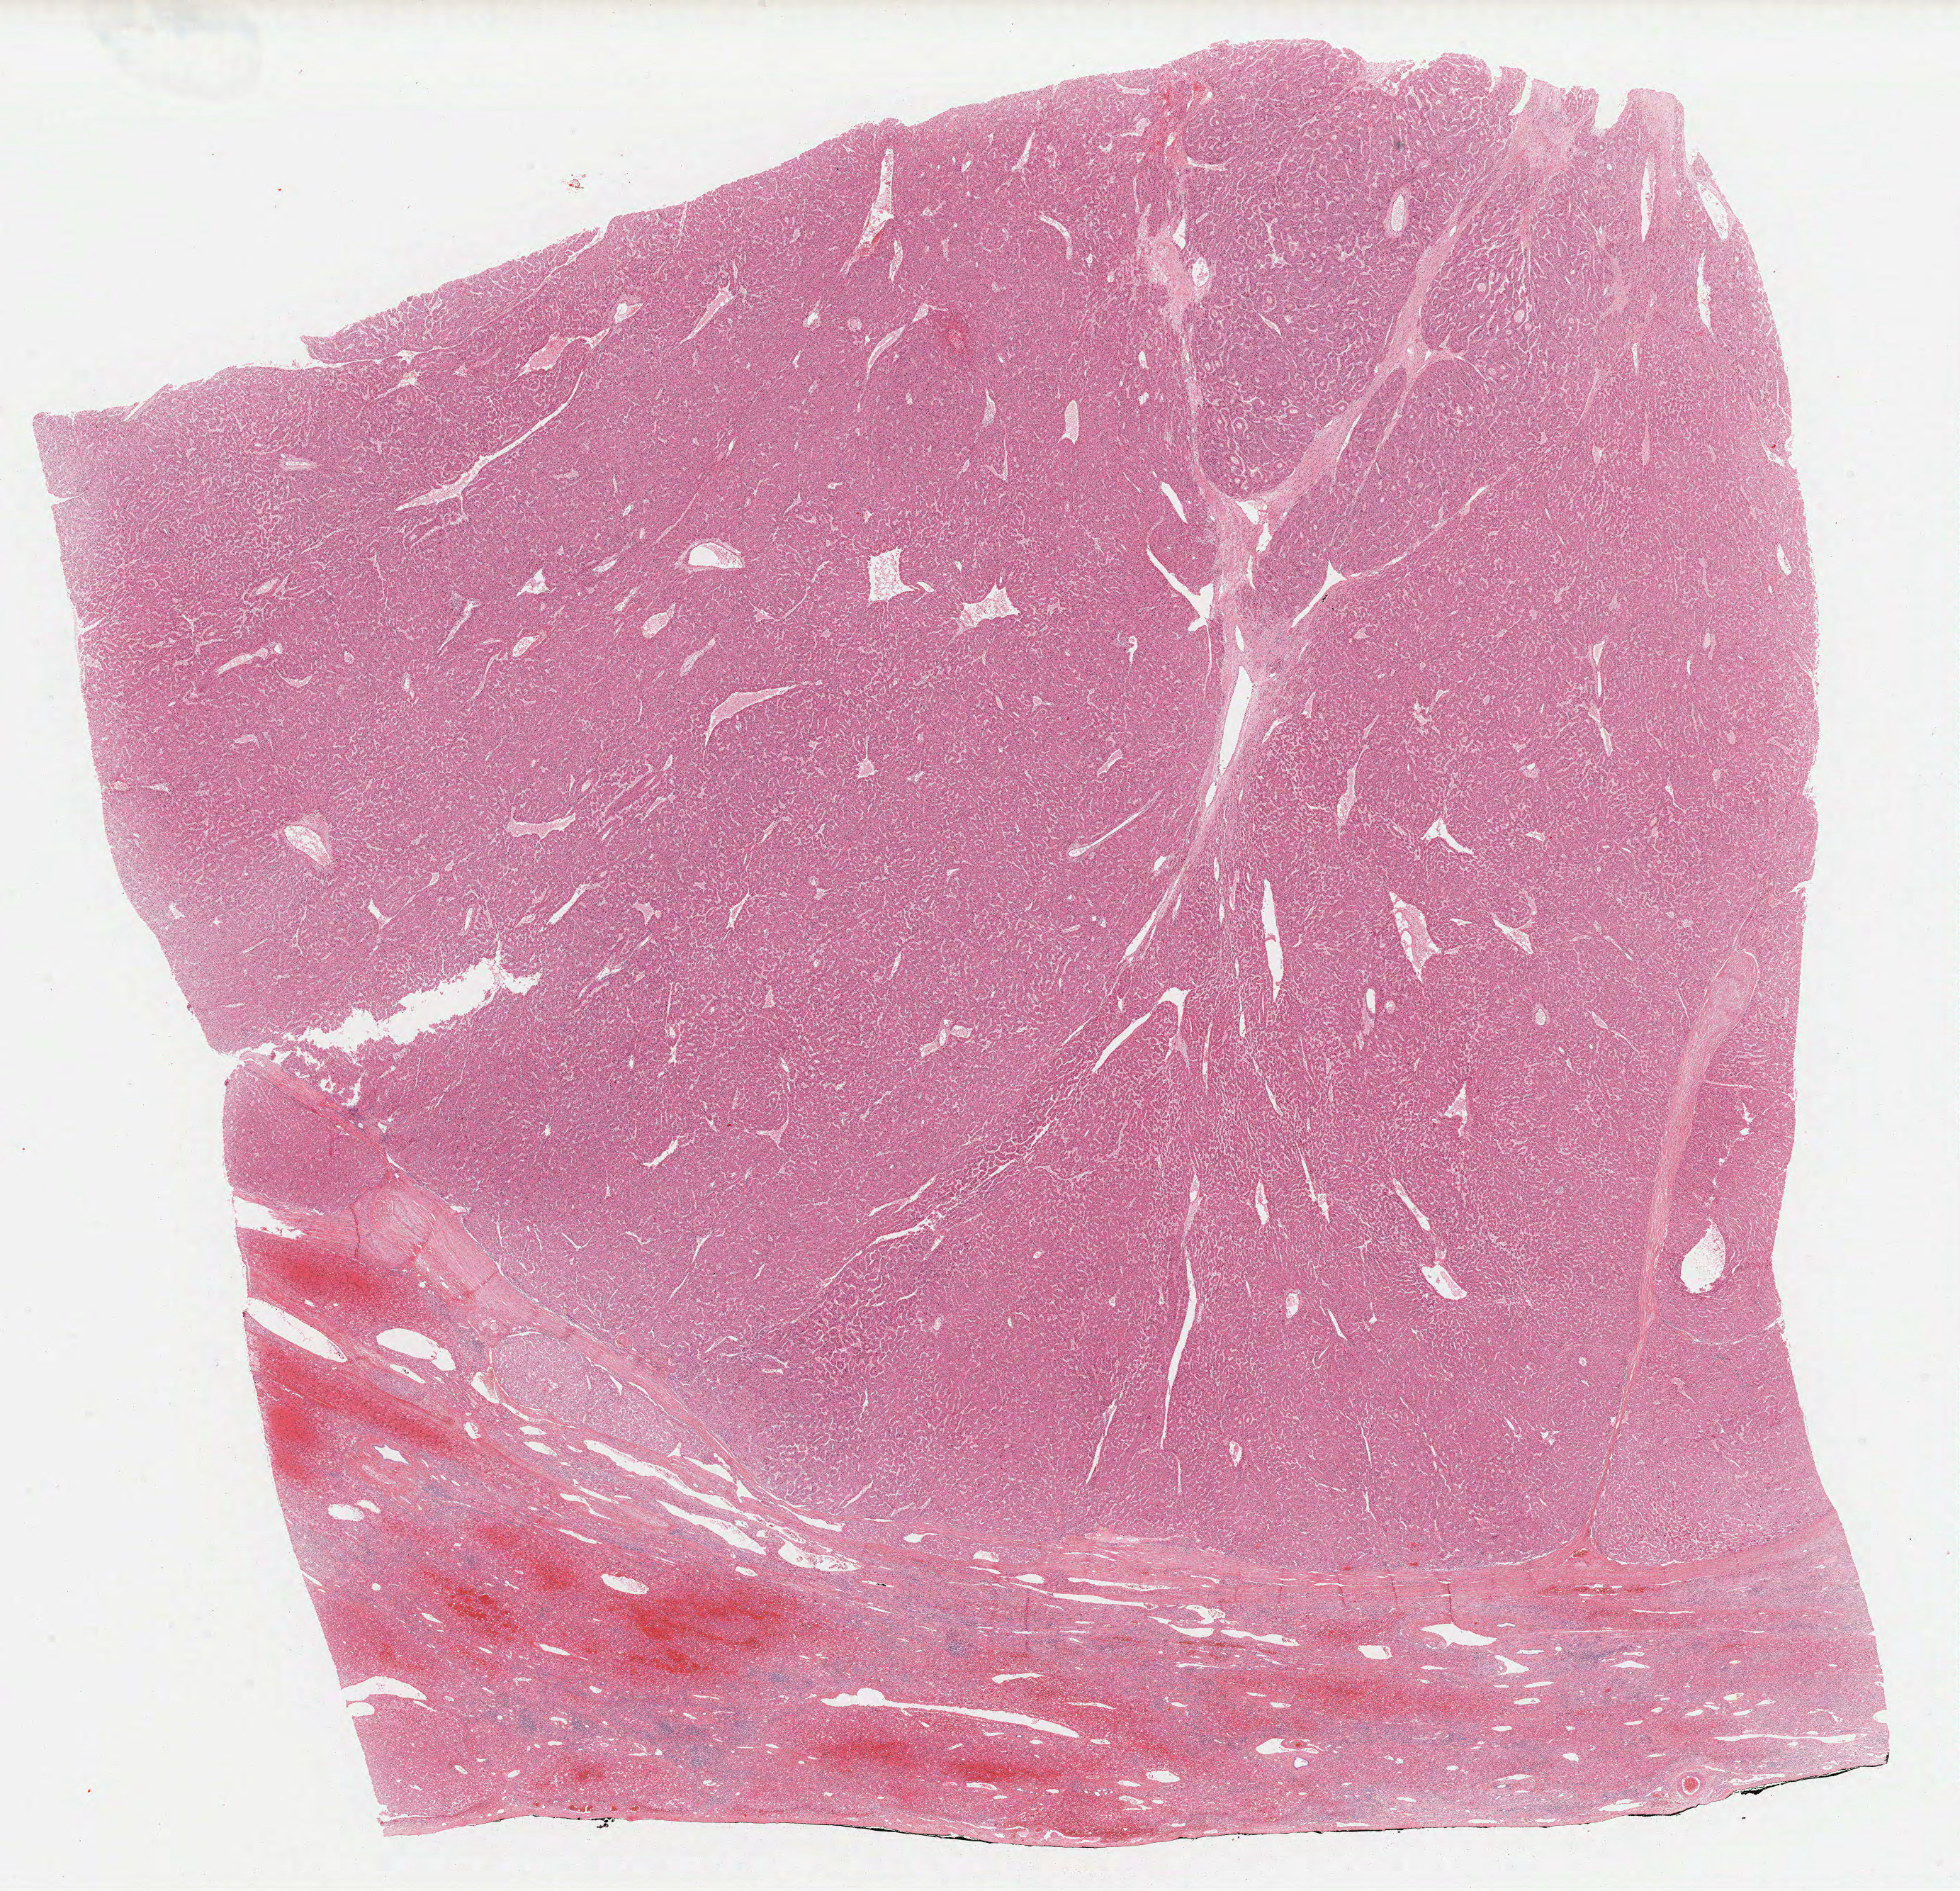
Hematoxylin and eosin (H&E) stained whole-slide image, low-resolution overview of the scanned area, about 21.9 x 21.1 mm (acquisition: 40x scan), formalin-fixed paraffin-embedded (FFPE) diagnostic section, sample: primary tumour, liver. Male, age 38 years at initial diagnosis.
Pathologic diagnosis: Hepatocellular carcinoma, NOS.